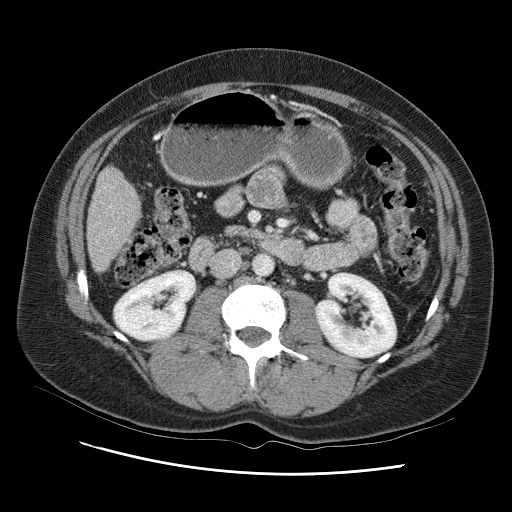
Contrast-enhanced abdominal CT (liver protocol), one axial slice. Slice 26 of 95 in the series (ordered by position). Reconstruction kernel STANDARD. 120 kVp. One of 2 acquisitions stored at this slice position. Soft-tissue window (W 400 / L 40 HU). 2.5 mm slice thickness. 512 × 512 image matrix, field of view 360 × 360 mm. Case-level facts recorded for this patient, not image findings: diagnosis: hepatocellular carcinoma (patient treated with transarterial chemoembolisation; whether this scan precedes or follows treatment is not stated here); TNM stage (as recorded): Stage-I; Child-Pugh class: B; tumour differentiation: moderately differentiated; tumour nodularity: uninodular.
Outlined on this slice (semi-automatically segmented with operator editing):
- liver parenchyma outside the tumour (the mass and vessels are separate outlines, so this box may not span the whole liver): bounding box (x1, y1, x2, y2) in pixels: (88, 150, 152, 270)
- liver vessels: (104, 198, 124, 249)